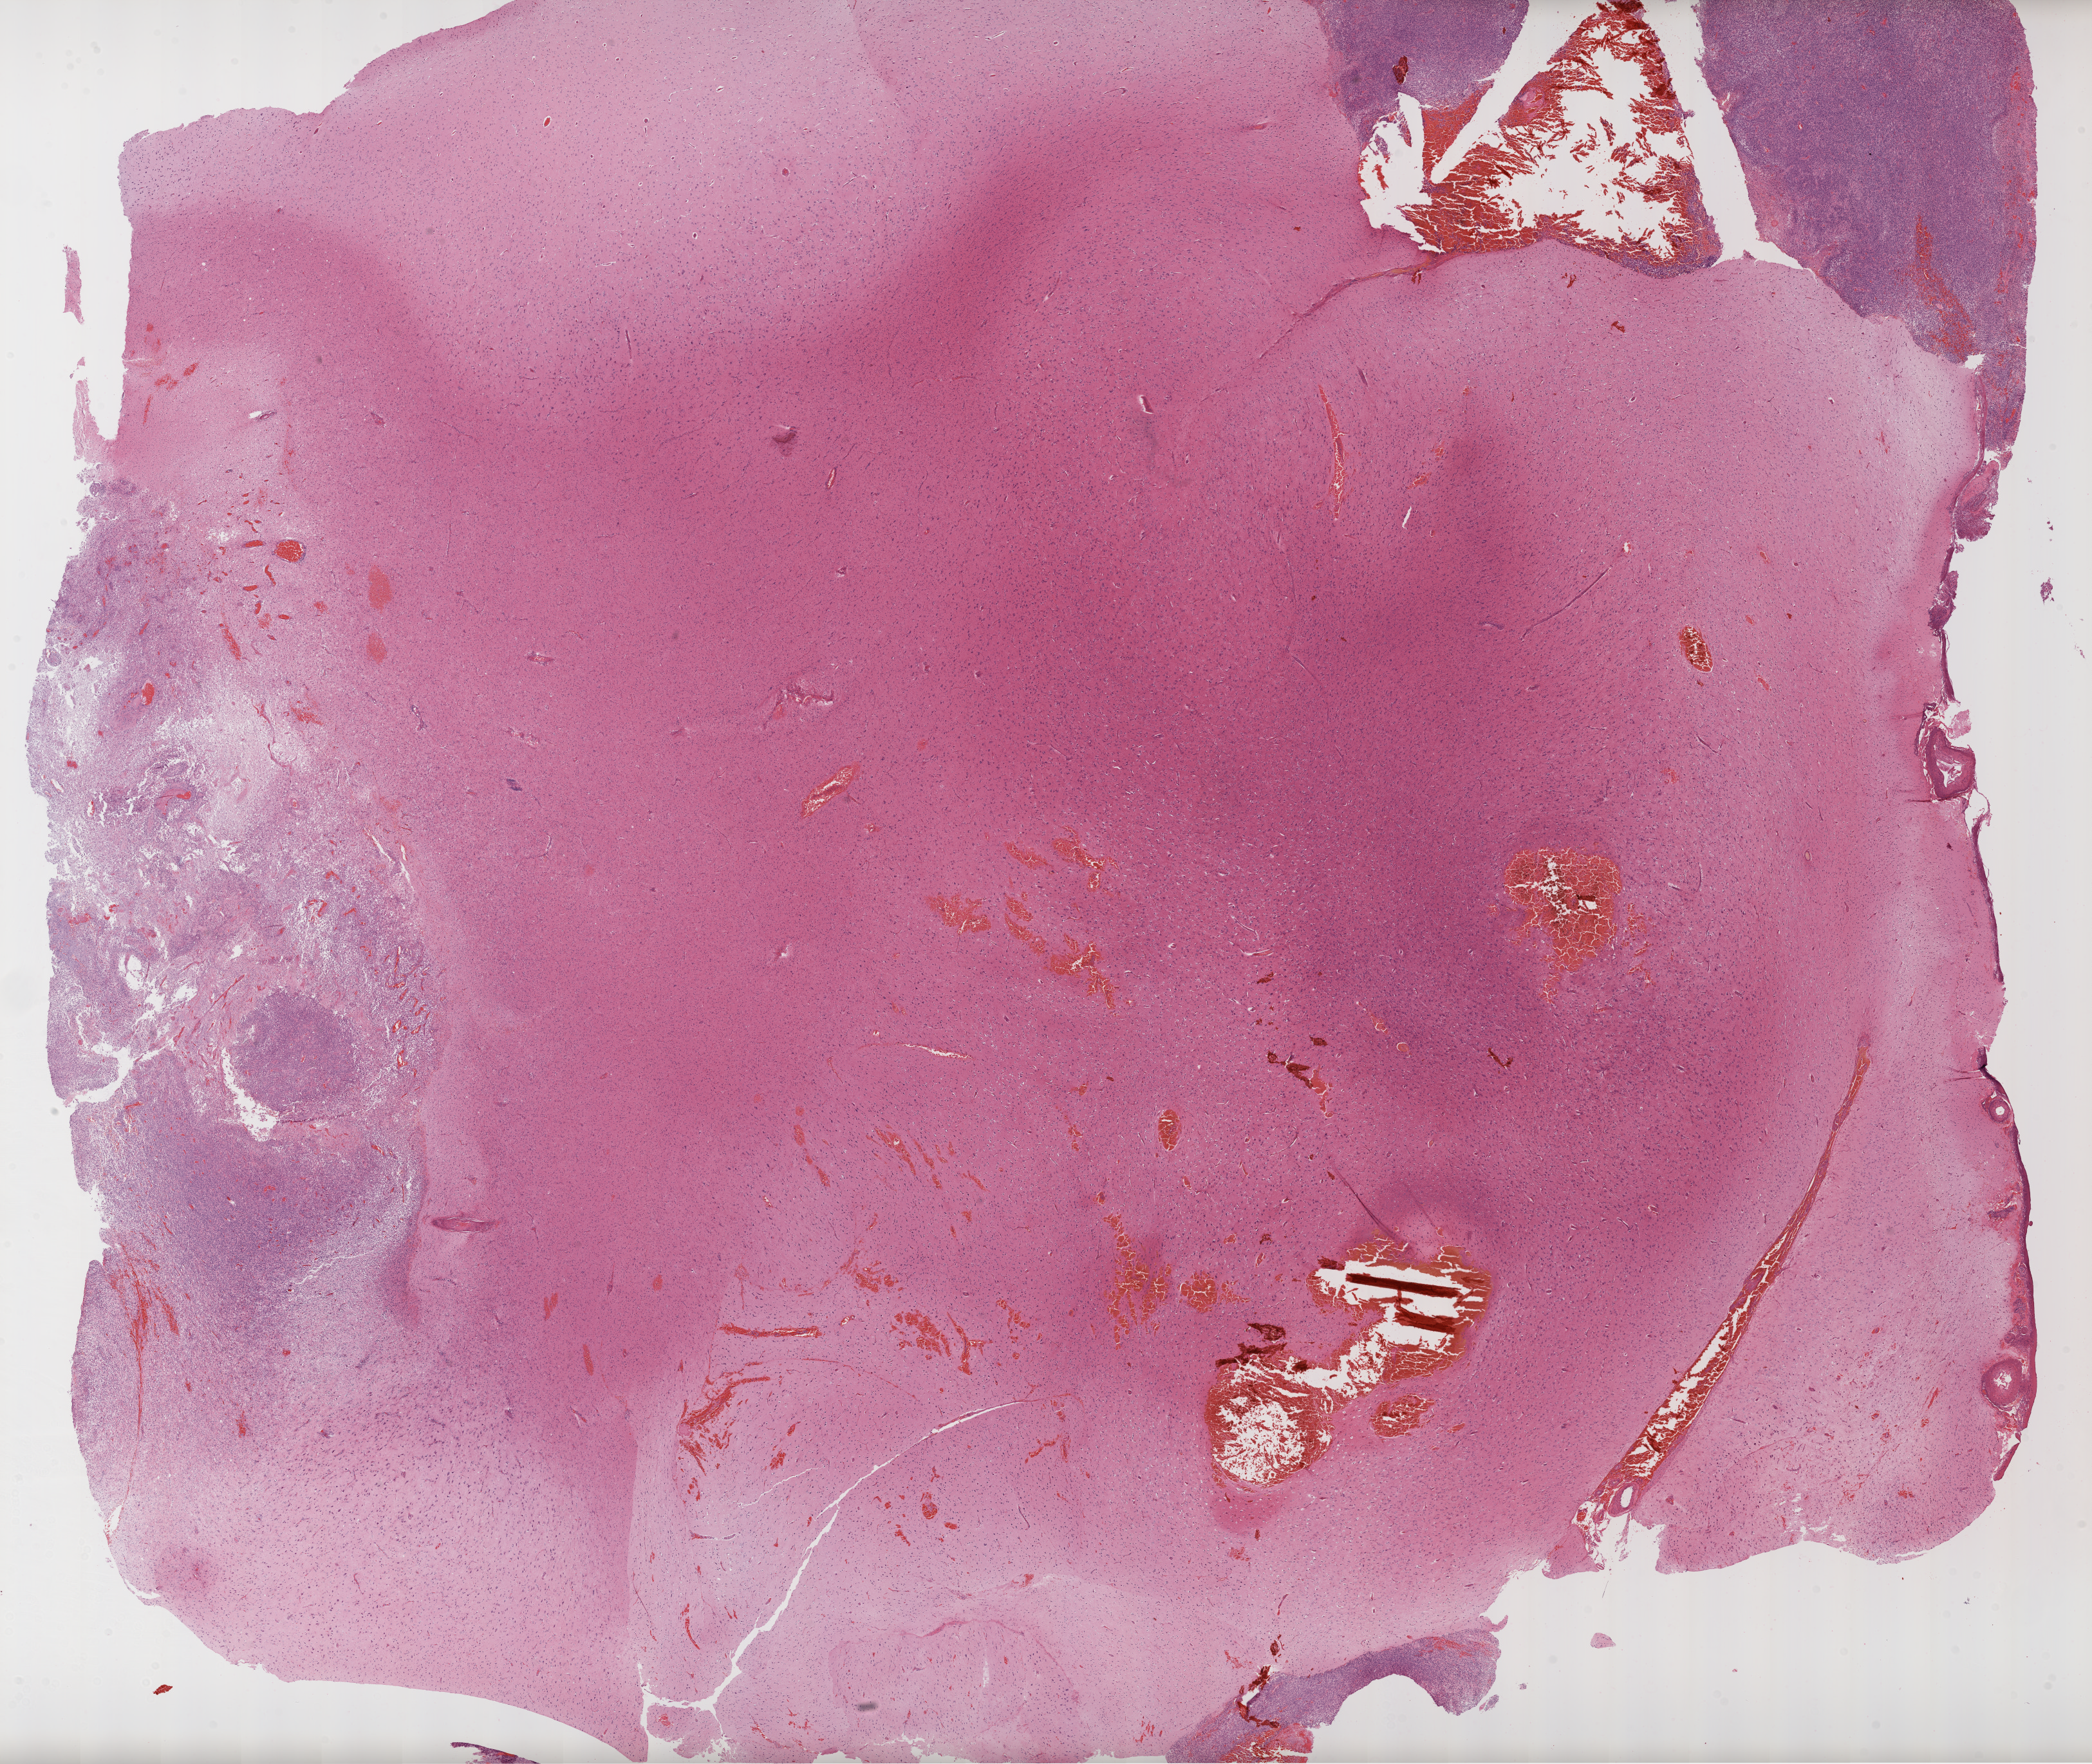
H&E-stained whole-slide image — shown as a low-resolution overview of the whole scanned area (about 26.1 x 22.0 mm). Formalin-fixed paraffin-embedded (FFPE) diagnostic section. Sample: primary tumour, brain. Female patient; age at initial diagnosis 59 years.
• diagnosis: Glioblastoma